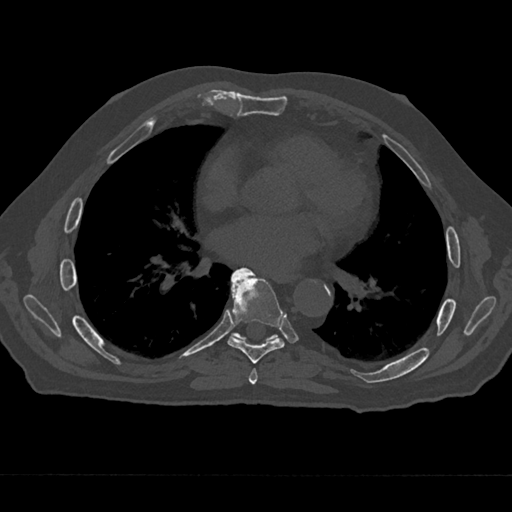
CT including the spine, one axial slice. Position 359 of 797 along the scan axis. Reconstruction kernel Br40s/3. Bone window (W 1800 / L 400 HU). 0.5 mm slice thickness. 512 × 512 image matrix. Male patient, age 75 years. From the clinical record (not read from this slice): primary cancer: renal.
Outlined on this slice (semi-automatic segmentation, software-assisted and operator-edited):
- T6 vertebra: box from (x=249, y=368) to (x=258, y=385) px
- T7 vertebra: (x=227, y=268)–(x=285, y=364)
- T8 vertebra: (x=231, y=333)–(x=278, y=342)